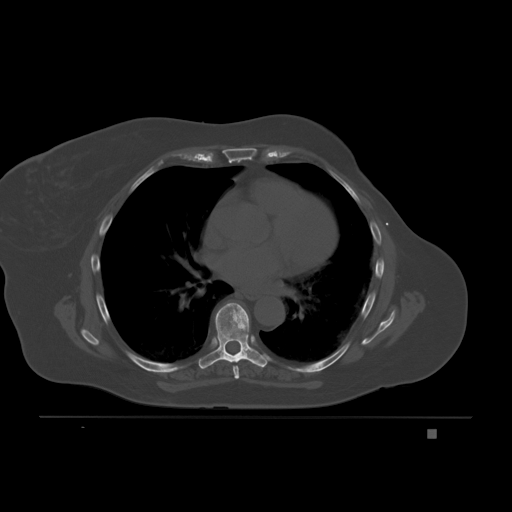
CT including the spine, one axial slice; position 129 of 221 along the scan axis; bone window (W 1800 / L 400 HU); 512 × 512 image matrix, field of view 474 × 474 mm. Female patient, age 63 years. From the clinical record (not read from this slice): primary cancer: breast.
Outlined on this slice (semi-automatically segmented with operator editing):
- T6 vertebra: bounding box (x1, y1, x2, y2) in pixels: (233, 365, 240, 379)
- T7 vertebra: (198, 302, 272, 369)